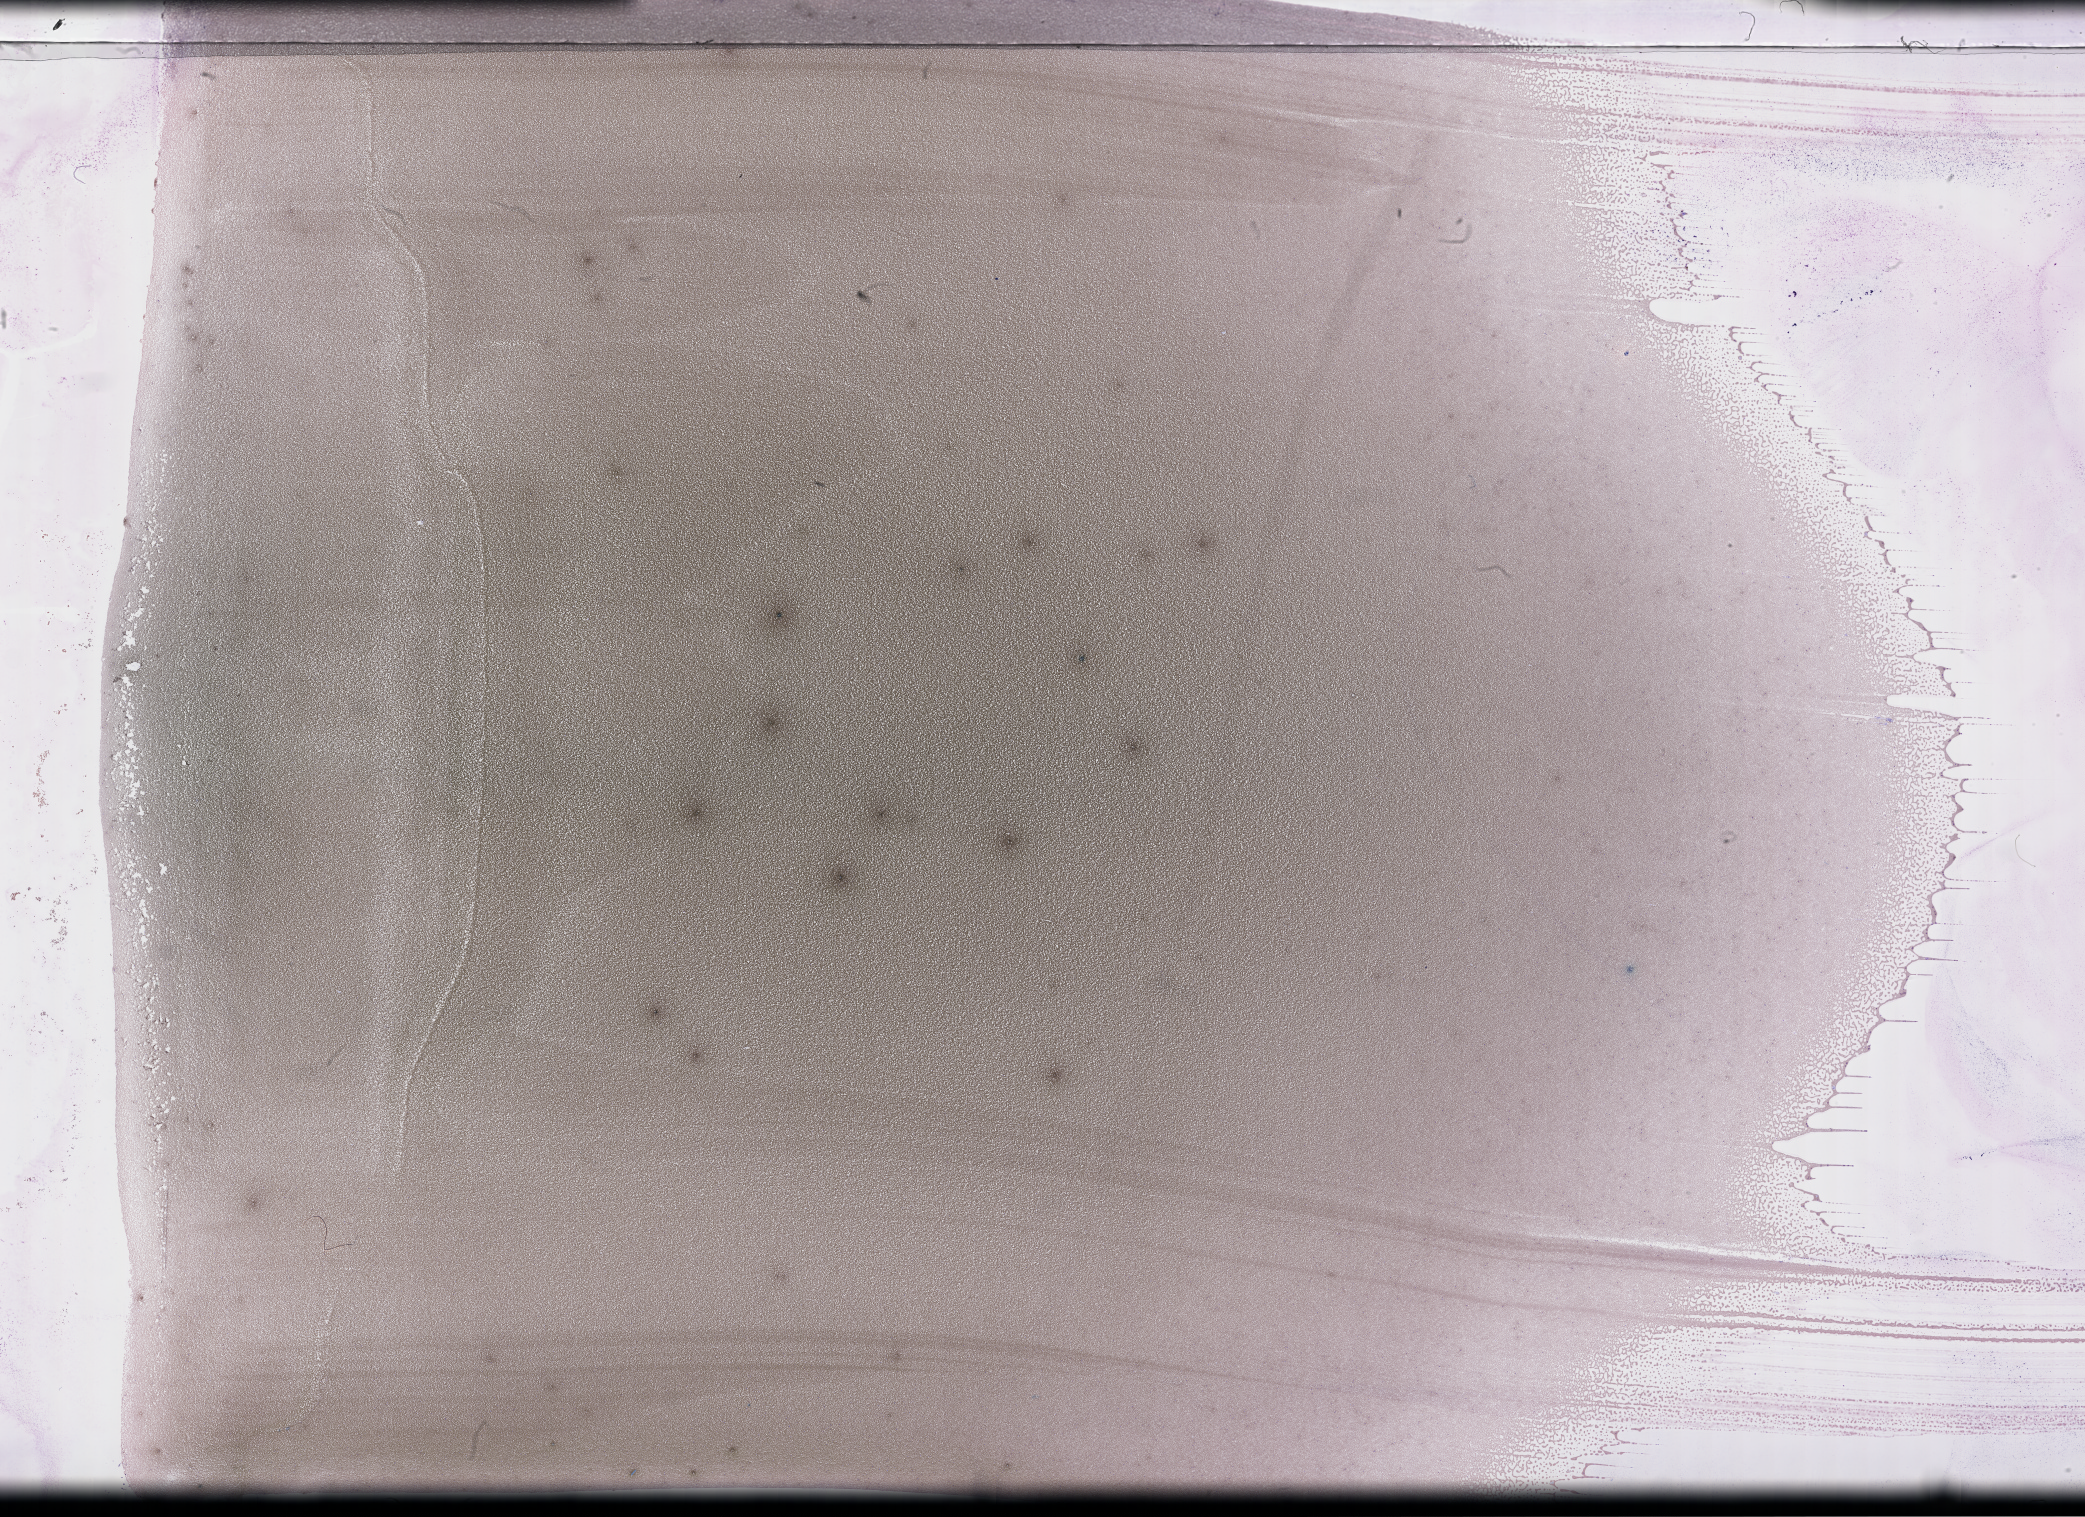
Whole-slide image of a whole blood smear, Wright-Giemsa stain — low-resolution overview of the scanned area, about 33.7 x 24.5 mm. Patient sex: female.
From a patient with: Plasma Cell Myeloma.